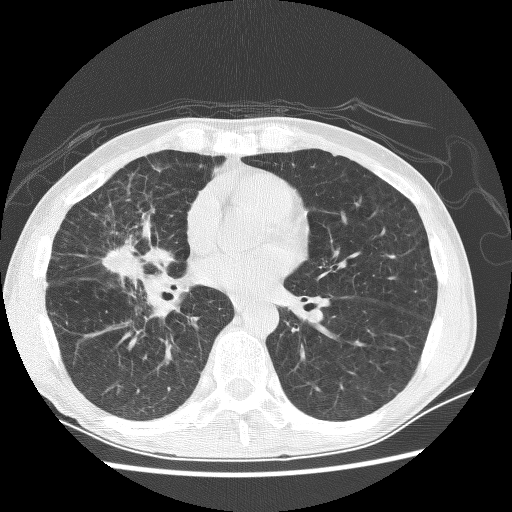
Low-dose screening chest CT, axial slice, baseline annual screen, lung window (W 1500 / L -600 HU), 2.5 mm slice thickness. Male participant, aged 67 years at enrolment. Current smoker at enrolment.
Expert reader's lesion annotation, bounding box [x1, y1, x2, y2] px = [79, 221, 174, 293]. The exam's reader record, not a measurement of the box and not confirmed to be the same lesion: non-calcified nodule or mass ≥4 mm, right middle lobe, 28 × 18 mm, spiculated (stellate) margins, soft tissue attenuation. Official screen result: positive, change unspecified: nodule(s) >= 4 mm or enlarging nodule(s), mass(es), or other non-specific abnormalities suspicious for lung cancer.